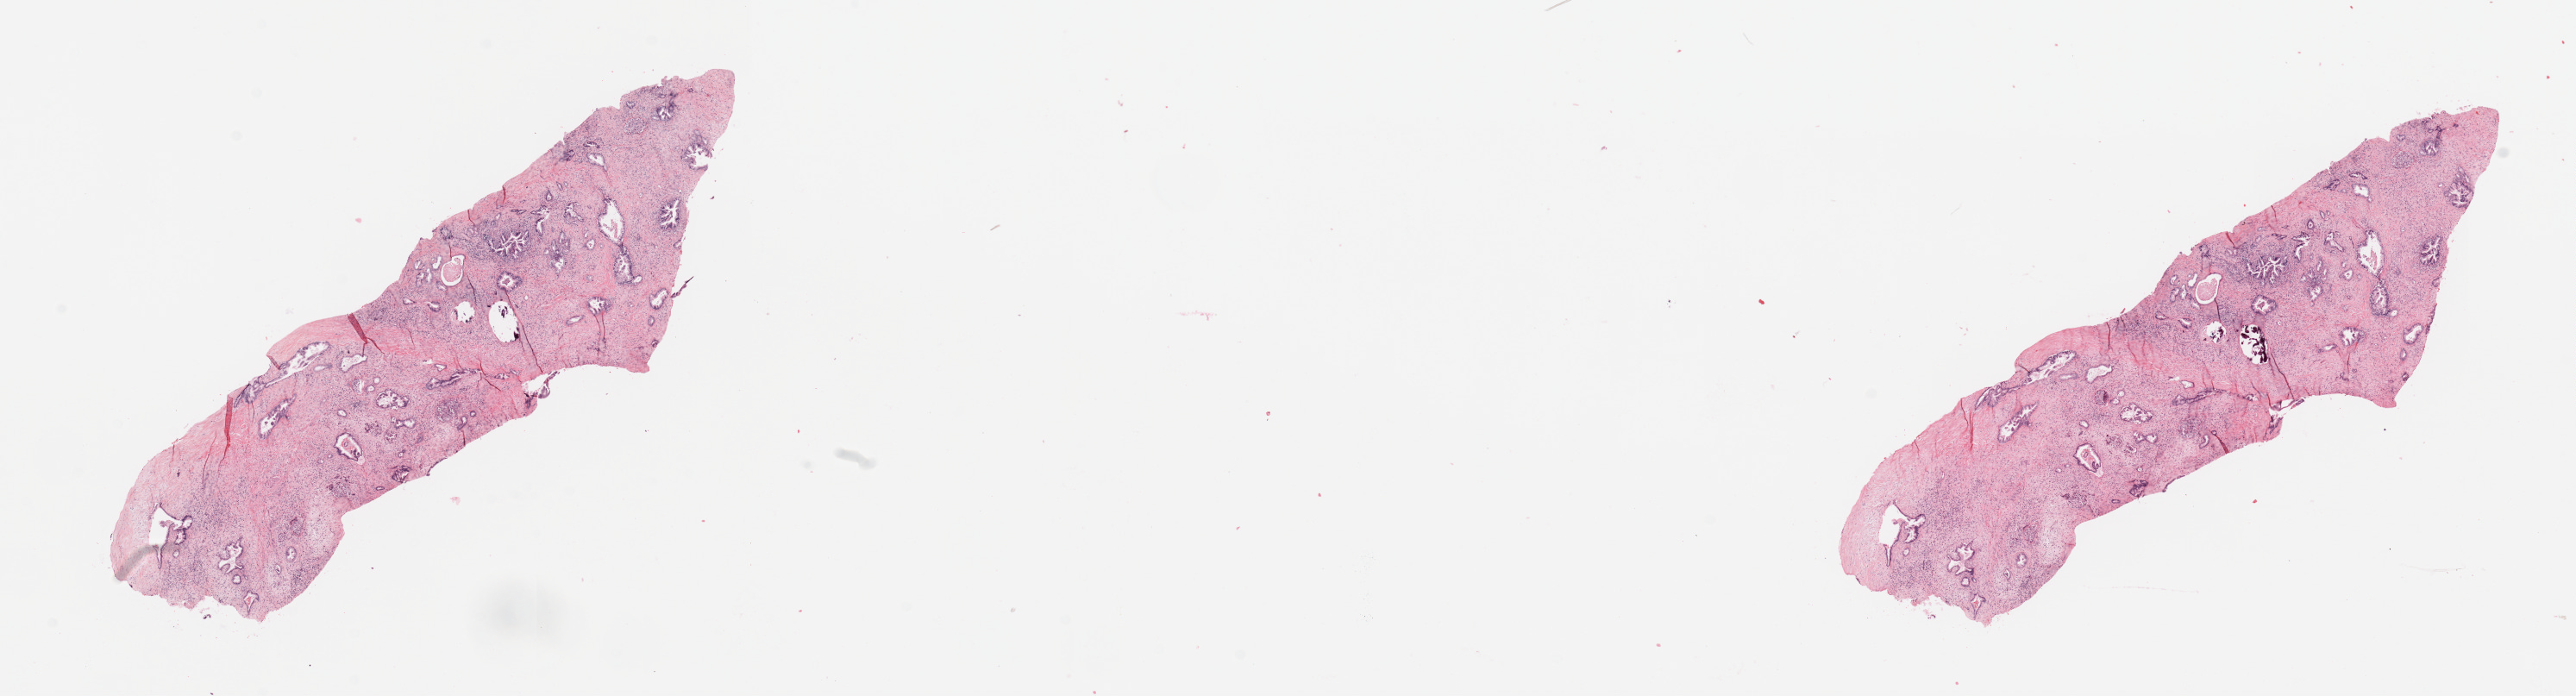
Digitized H&E tissue section (whole slide) — whole scanned area (about 23.6 x 6.4 mm, from a 20x scan) shown as a low-resolution overview; pancreas, tumour tissue. Male, 71 y/o. Histologic grade: G2 (moderately differentiated).
Primary tumour site (as recorded): body. Histologic diagnosis: Infiltrating duct carcinoma, NOS. AJCC pathologic stage: IIB.